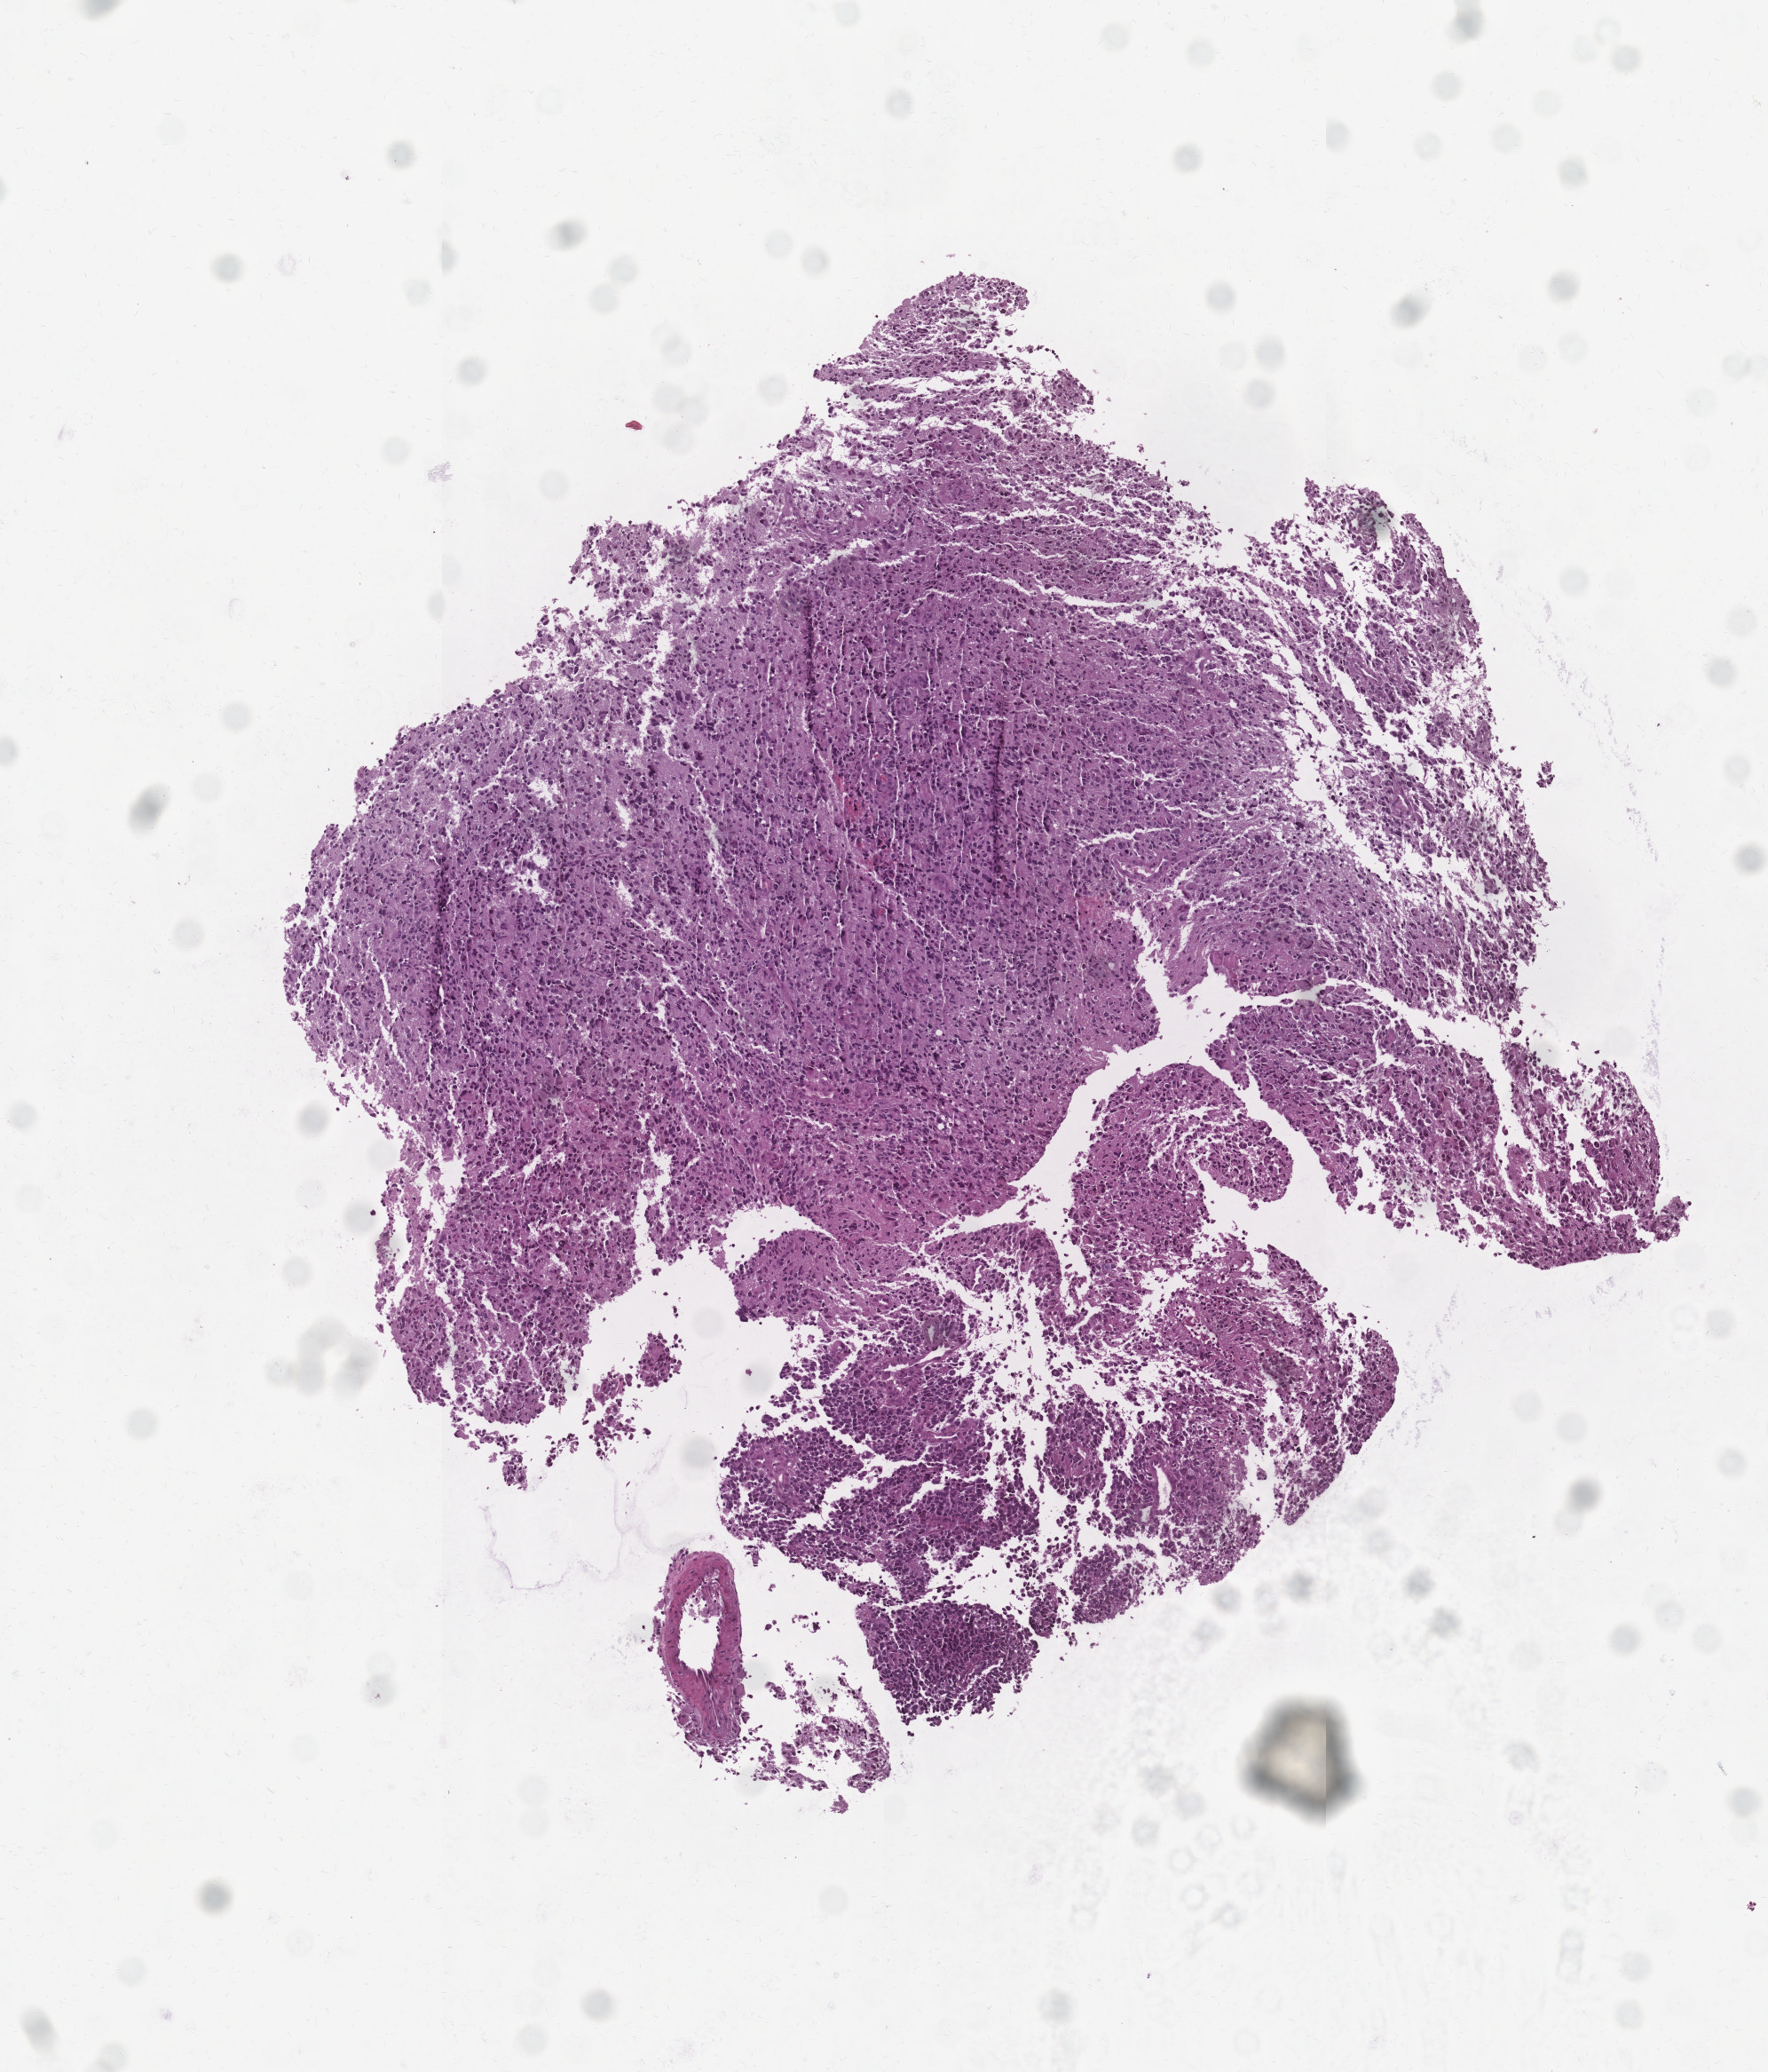
Hematoxylin and eosin (H&E) stained whole-slide image — a low-resolution overview of the entire scanned area, about 4.0 x 4.7 mm (from a 20x scan), tumour tissue sample, sampled site: brain. Male, 59 y/o. Composition of this section per pathologist review: tumour nuclei 80%, necrosis 7%.
Histologic diagnosis: Glioblastoma. Primary tumour site (as recorded): temporal lobe.